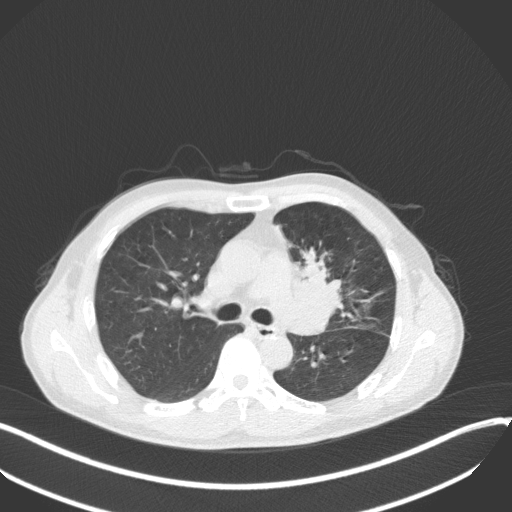
Chest CT, one axial slice. Position 211 of 411 along the scan axis. Reconstruction kernel B31f. Lung window (W 1500 / L -600 HU). 1 mm slice thickness. 512 × 512 image matrix, field of view 400 × 400 mm. Patient: male, 56 years. Case-level facts recorded for this patient, not image findings: clinical TNM (as recorded): T2a N0 M0.
Structures marked on this image (bounding box drawn by a radiologist):
- lung tumour (recorded histology: squamous cell carcinoma): bounding box [x1, y1, x2, y2] px = [292, 248, 348, 334]